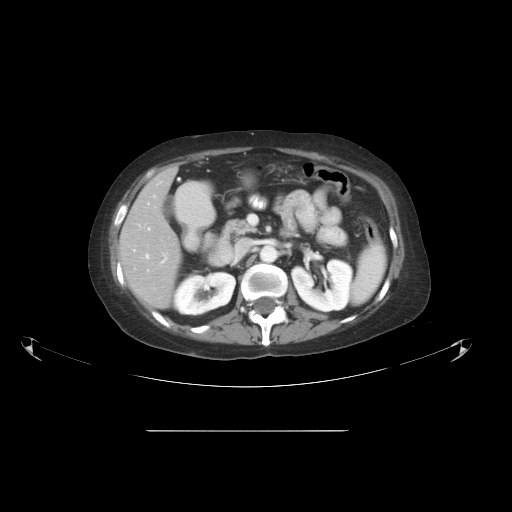
Contrast-enhanced abdominal CT, one axial slice; position 27 of 51 along the scan axis; 120 kVp; intravenous contrast given; soft-tissue window (W 400 / L 40 HU); 5 mm slice thickness; 512 × 512 image matrix, field of view 475 × 475 mm. Female patient, age 48 years. Case-level facts recorded for this patient, not image findings: diagnosis: colorectal cancer liver metastases, imaged before liver resection; multiple liver metastases: yes; largest metastasis: 1 cm; disease in both lobes: no.
Structures marked on this image (manually delineated by an expert):
- hepatic veins: bounding box (x1, y1, x2, y2) in pixels: (146, 196, 167, 262)
- liver: (120, 169, 182, 308)
- planned liver remnant (the part of the liver to remain after resection): (120, 169, 182, 308)
- portal vein (with intrahepatic branches): (134, 228, 150, 251)